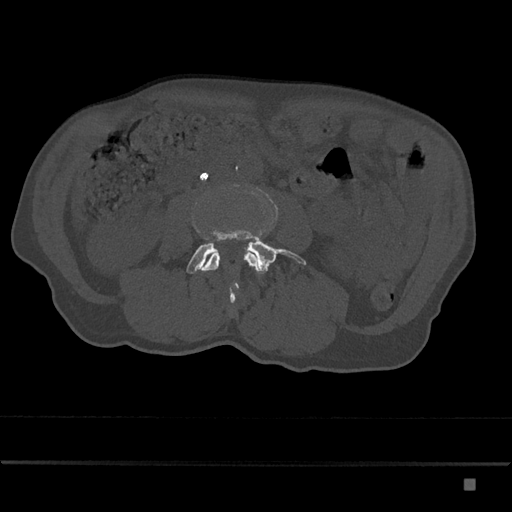
CT including the spine, one axial slice. Slice 367 of 797 in the series (ordered by position). Reconstruction kernel Br40s/3. 120 kVp. Bone window (W 1800 / L 400 HU). 0.5 mm slice thickness. 512 × 512 image matrix, field of view 390 × 390 mm. Male patient, age 72 years. From the clinical record (not read from this slice): primary cancer: prostate.
Outlined on this slice (semi-automatic segmentation, software-assisted and operator-edited):
- L3 vertebra: bounding box (x1, y1, x2, y2) in pixels: (202, 253, 258, 289)
- L4 vertebra: (186, 230, 306, 302)